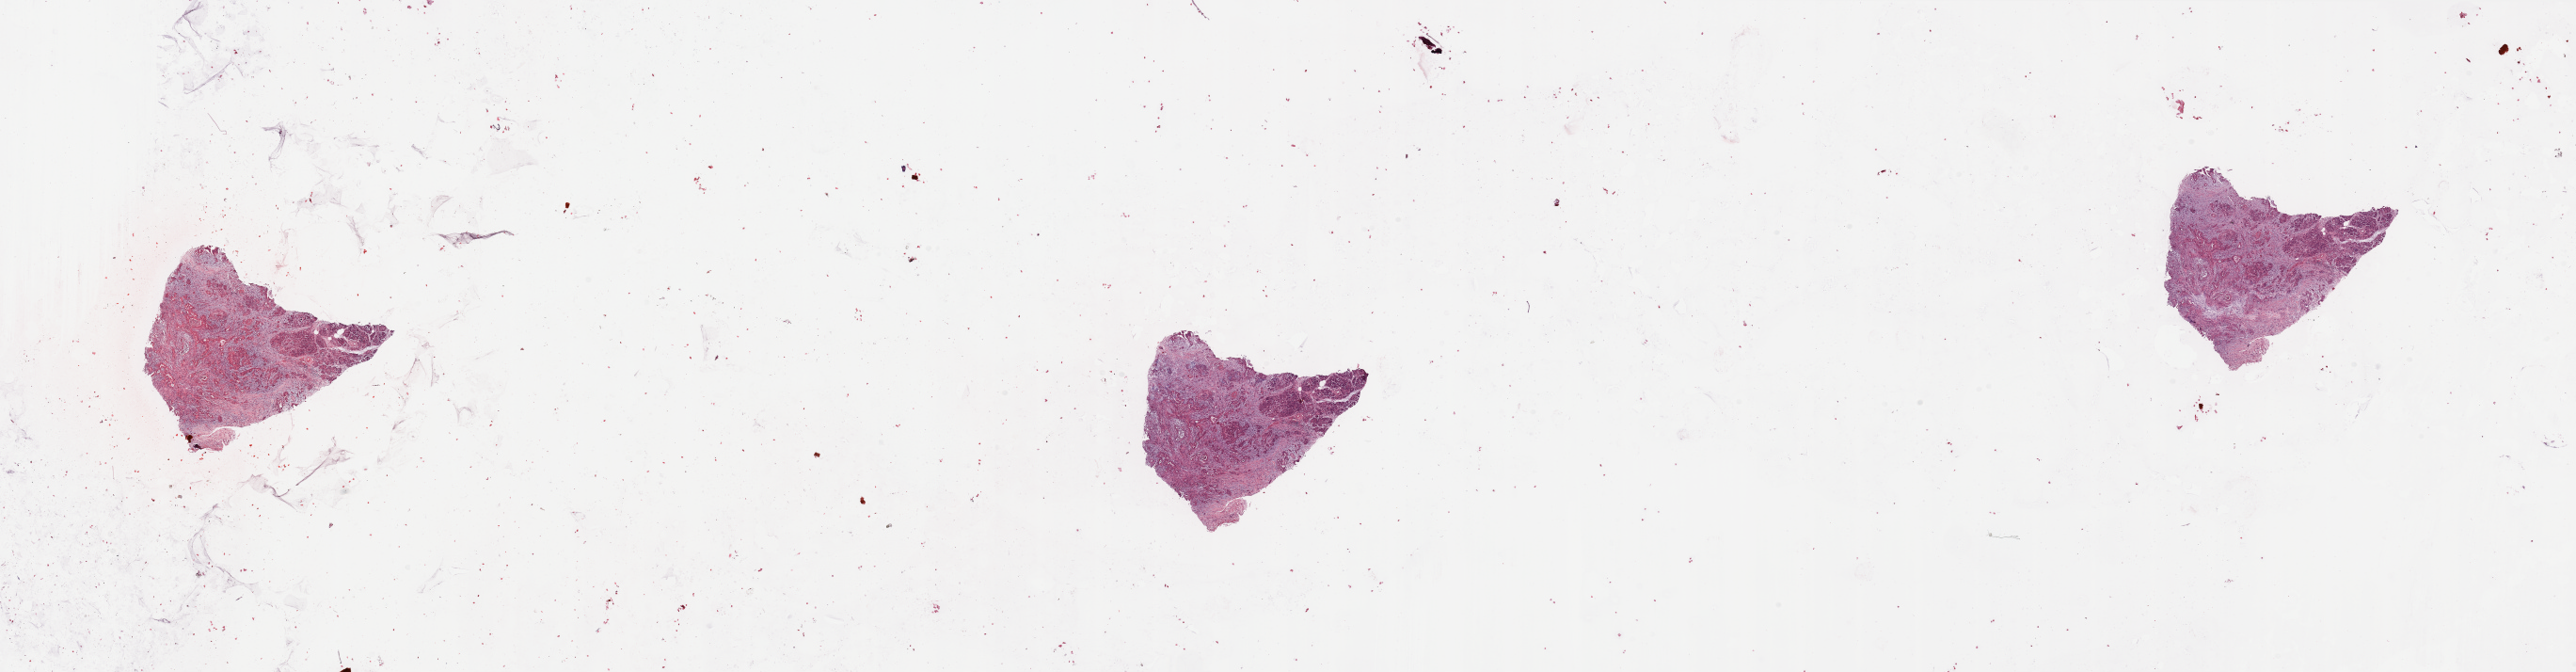
H&E whole-slide image, a low-resolution overview of the entire scanned area, about 43.3 x 11.3 mm (from a 20x scan), tumour tissue sample, sampled site: pancreas. Female, 74 y/o. Histologic grade: G3 (poorly differentiated). Pathologist review of this section (percent, as recorded): tumour nuclei 30%, necrosis 2%.
- primary tumour site (as recorded): head
- AJCC pathologic stage: III
- histologic diagnosis: Infiltrating duct carcinoma, NOS